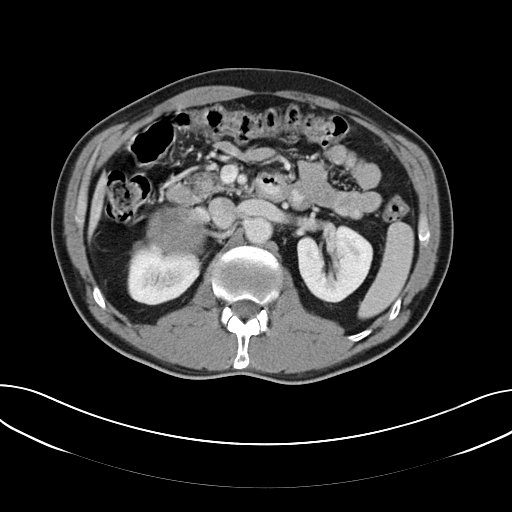
Contrast-enhanced abdominal CT, one axial slice; slice 29 of 61 in the series (ordered by position); reconstruction kernel B40f; 120 kVp; intravenous contrast given; soft-tissue window (W 400 / L 40 HU); 5 mm slice thickness; 512 × 512 image matrix, field of view 372 × 372 mm. Male patient, age 57 years. Case-level facts recorded for this patient, not image findings: diagnosis: adrenocortical carcinoma; tumour side: right adrenal; tumour size at pathology: 11.2 cm; Ki-67 index: 10 %; stage (as recorded): 3.
Outlined on this slice (semi-automatic segmentation, software-assisted and operator-edited):
- mass: bounding box <145,206,205,252> (left, top, right, bottom; pixels)